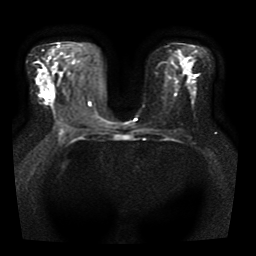
Breast MRI, one axial slice. Position 23 of 41 along the scan axis. Diffusion-weighted series; image 2 of 4 stored at this slice position (different b-values; order by instance number). 1.5 T. 5 mm slice thickness. 256 × 256 image matrix, field of view 330 × 330 mm. Female patient.
Outlined on this slice (expert manual segmentation):
- tumour on diffusion-weighted imaging: box from (x=45, y=97) to (x=51, y=101) px